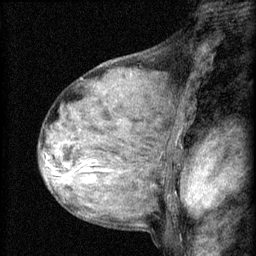
Breast MRI (dynamic contrast-enhanced), one sagittal slice. 3 images stored at this slice position (order not interpretable as contrast timing). 1.5 T. TE 4.2 ms, TR 8.2 ms. 256 × 256 image matrix. Patient: female, 48 years.
Outlined on this slice (semi-automatic segmentation, software-assisted and operator-edited):
- analysis volume of interest (the breast-tissue region the enhancement analysis was run in; not a lesion): bounding box [x1, y1, x2, y2] px = [54, 138, 133, 191]
- tumour enhancement mask (voxels above the 70 % enhancement threshold inside the analysis volume of interest): [54, 160, 93, 177]